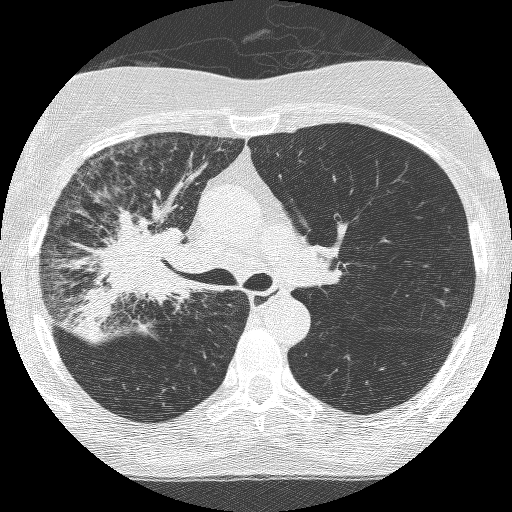
Chest CT (low-dose screening protocol), one axial image; third annual screen; lung window (W 1500 / L -600 HU); lung (sharp) reconstruction kernel (BONE); slice 167 of 253 in the series. Female, age 64 years at enrolment.
Lesion marked by an expert reader, bounding box (x1, y1, x2, y2) in pixels: (83, 210, 204, 331). Screening reader's record for this exam (one nodule recorded; not confirmed to be the boxed lesion): non-calcified nodule or mass ≥4 mm, right upper lobe, 49 × 43 mm, spiculated (stellate) margins, soft tissue attenuation, pre-existing on the prior screen: yes; interval growth: yes. Participant outcome: lung cancer diagnosed 7 days after this screen — adenocarcinoma, NOS, right upper lobe, right middle lobe, right hilum, stage IV (AJCC 6th edition), 85 mm at pathology.